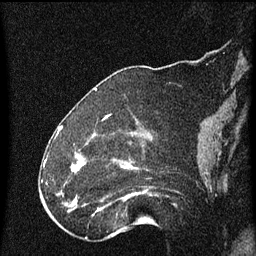
Breast MRI (dynamic contrast-enhanced), one sagittal slice; dynamic contrast-enhanced series, image 2 of 4 at this slice position (ordered by acquisition); 1.5 T; TE 4.2 ms, TR 8 ms; 2 mm slice thickness; 256 × 256 image matrix, field of view 180 × 180 mm. Patient: female, 52 years.
Structures marked on this image (semi-automatically segmented with operator editing):
- analysis volume of interest (the breast-tissue region the enhancement analysis was run in; not a lesion): box from (x=73, y=148) to (x=154, y=219) px
- tumour enhancement mask (voxels above the 70 % enhancement threshold inside the analysis volume of interest): (x=73, y=164)–(x=133, y=211)